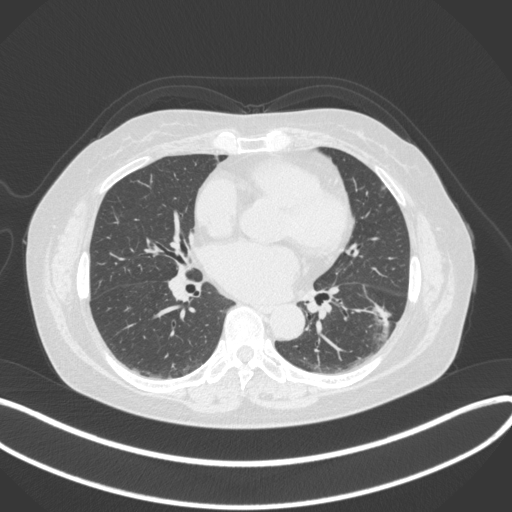
Chest CT, one axial slice. Slice 169 of 373 in the series (ordered by position). Reconstruction kernel B31f. Lung window (W 1500 / L -600 HU). 1 mm slice thickness. 512 × 512 image matrix. Patient: female, 67 years. From the clinical record (not read from this slice): clinical TNM (as recorded): T1c N0 M0.
Outlined on this slice (bounding box drawn by a radiologist):
- lung tumour (recorded histology: adenocarcinoma): box from (x=358, y=290) to (x=395, y=344) px